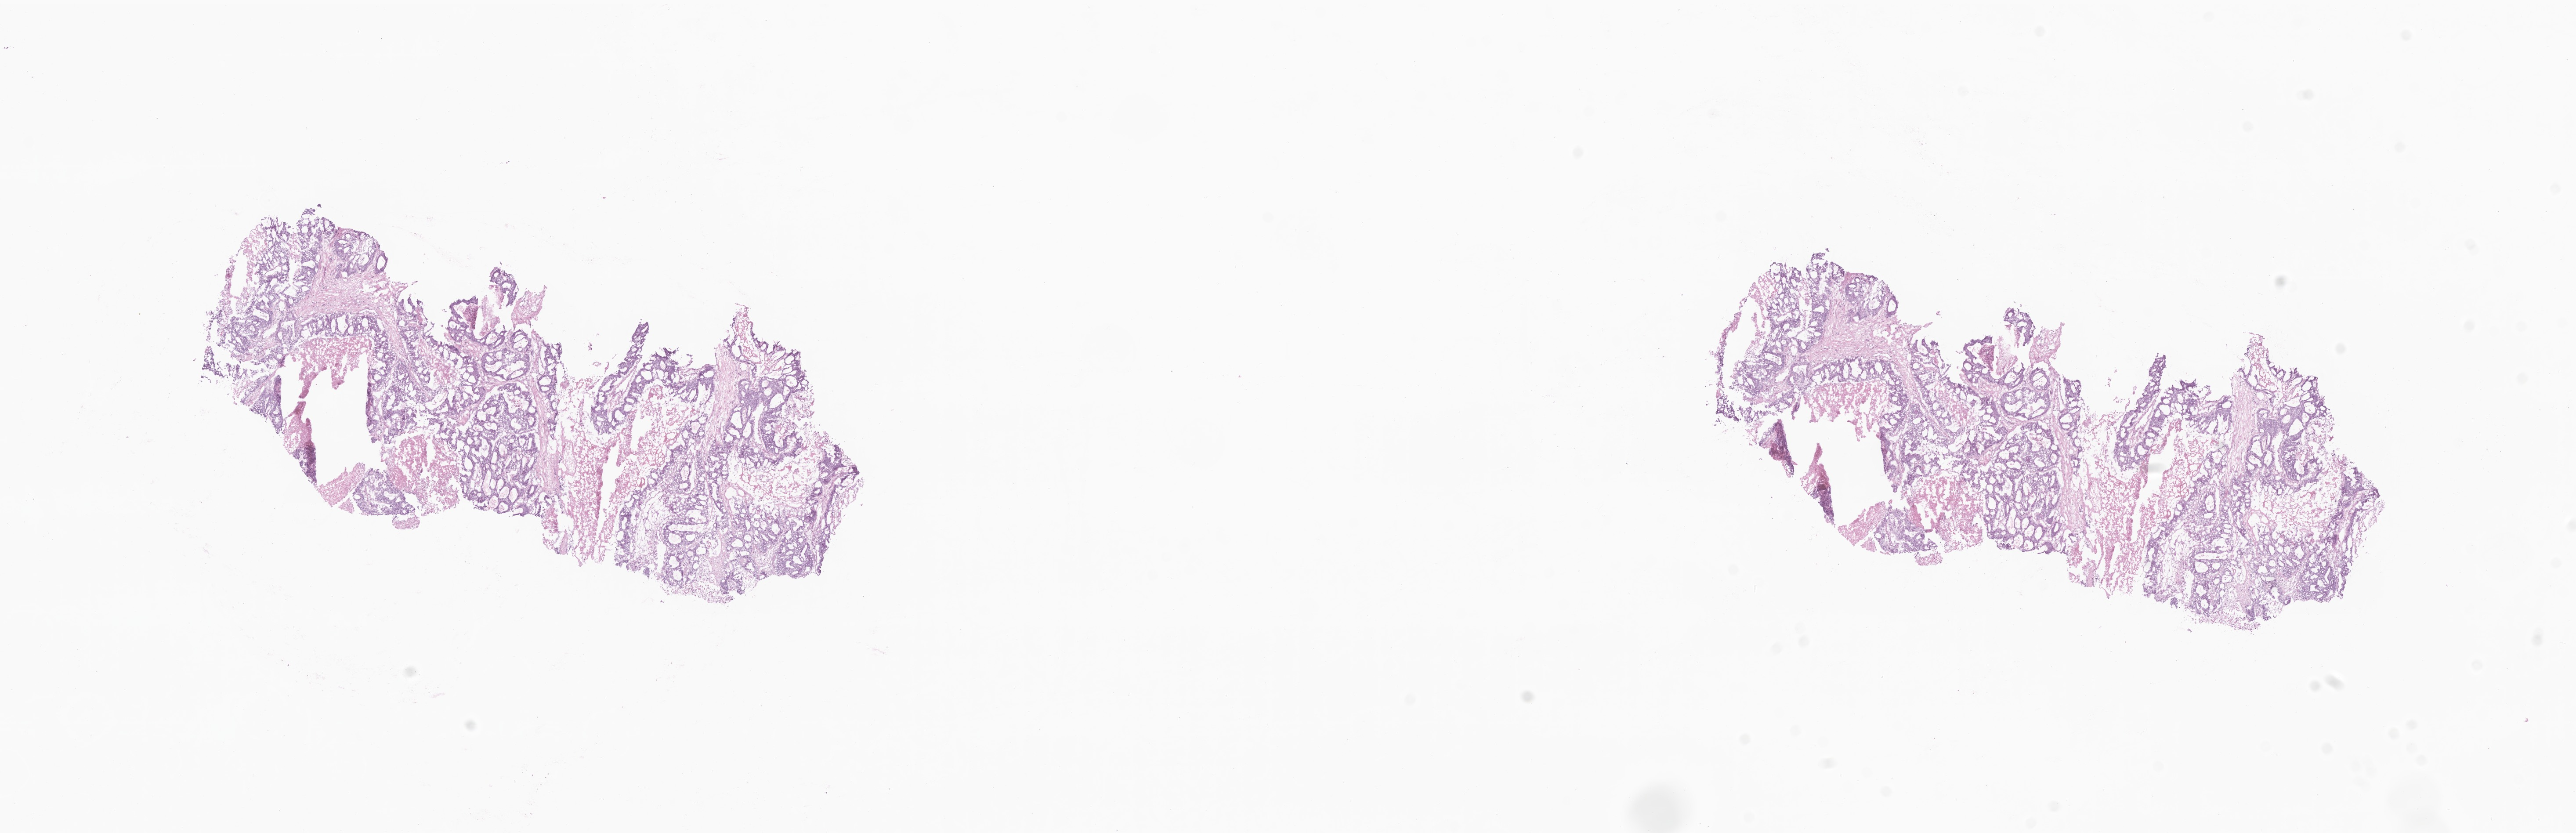
H&E whole-slide image, whole scanned area (about 24.7 x 8.0 mm) shown as a low-resolution overview; frozen section (tissue freezing medium); specimen: metastatic tumor tissue, resected from liver. Male patient; age at initial diagnosis 61 years. Composition of this section per pathologist review: tumor cells 75%, tumor nuclei 75%, stromal cells 15%, necrosis 10%, normal cells 0%. Inflammatory infiltration, as recorded: lymphocyte infiltration 4%, monocyte infiltration 1%, neutrophil infiltration 6%.
Patient diagnosis (primary): Adenocarcinoma, NOS.